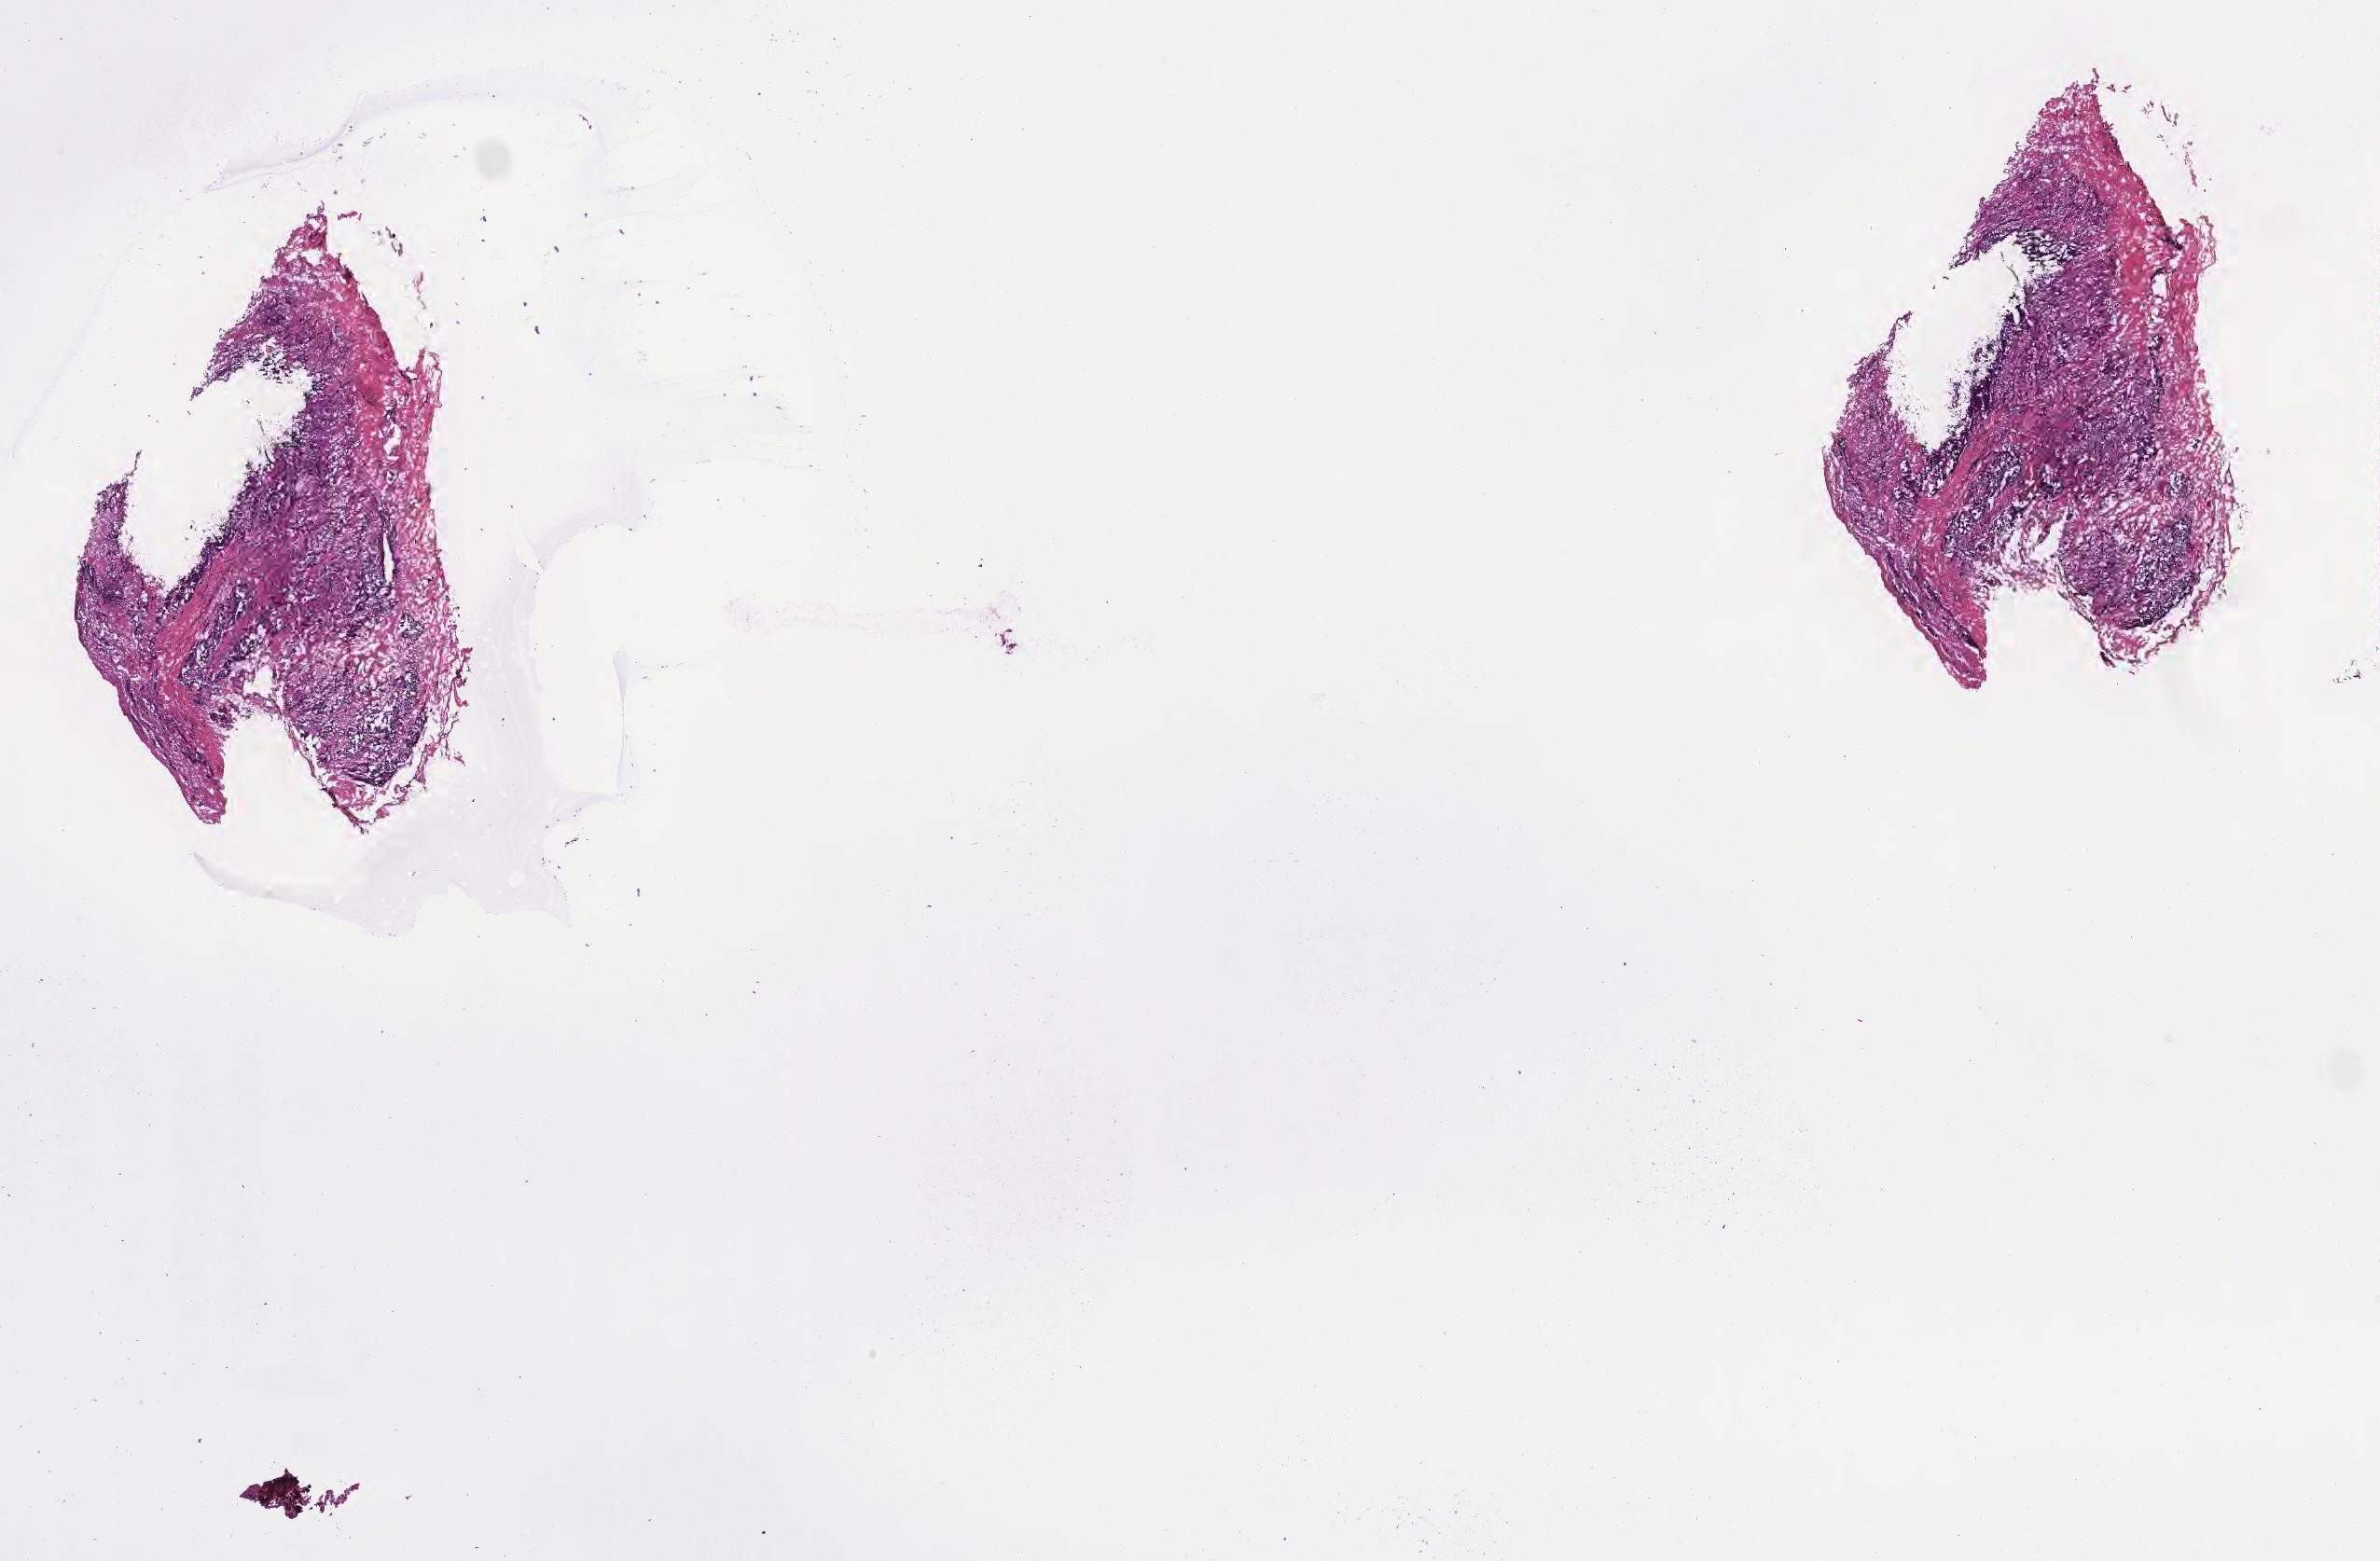
Whole-slide image, H&E stain of tumor tissue from the abdomen — a low-resolution overview of the entire scanned area, about 20.6 x 13.5 mm, frozen section. Patient female; age 116 months (9 years 8 months).
Diagnosis: Alveolar rhabdomyosarcoma.